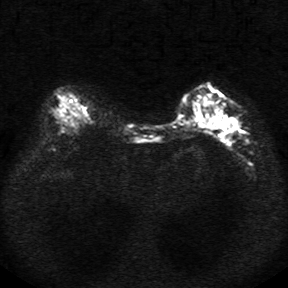
Breast MRI, one axial slice. Position 11 of 34 along the scan axis. Diffusion-weighted series; image 2 of 4 stored at this slice position (different b-values; order by instance number). 1.5 T. 288 × 288 image matrix, field of view 340 × 340 mm. Female patient.
Structures marked on this image (expert manual segmentation):
- tumour on diffusion-weighted imaging: bounding box <194,115,237,132> (left, top, right, bottom; pixels)